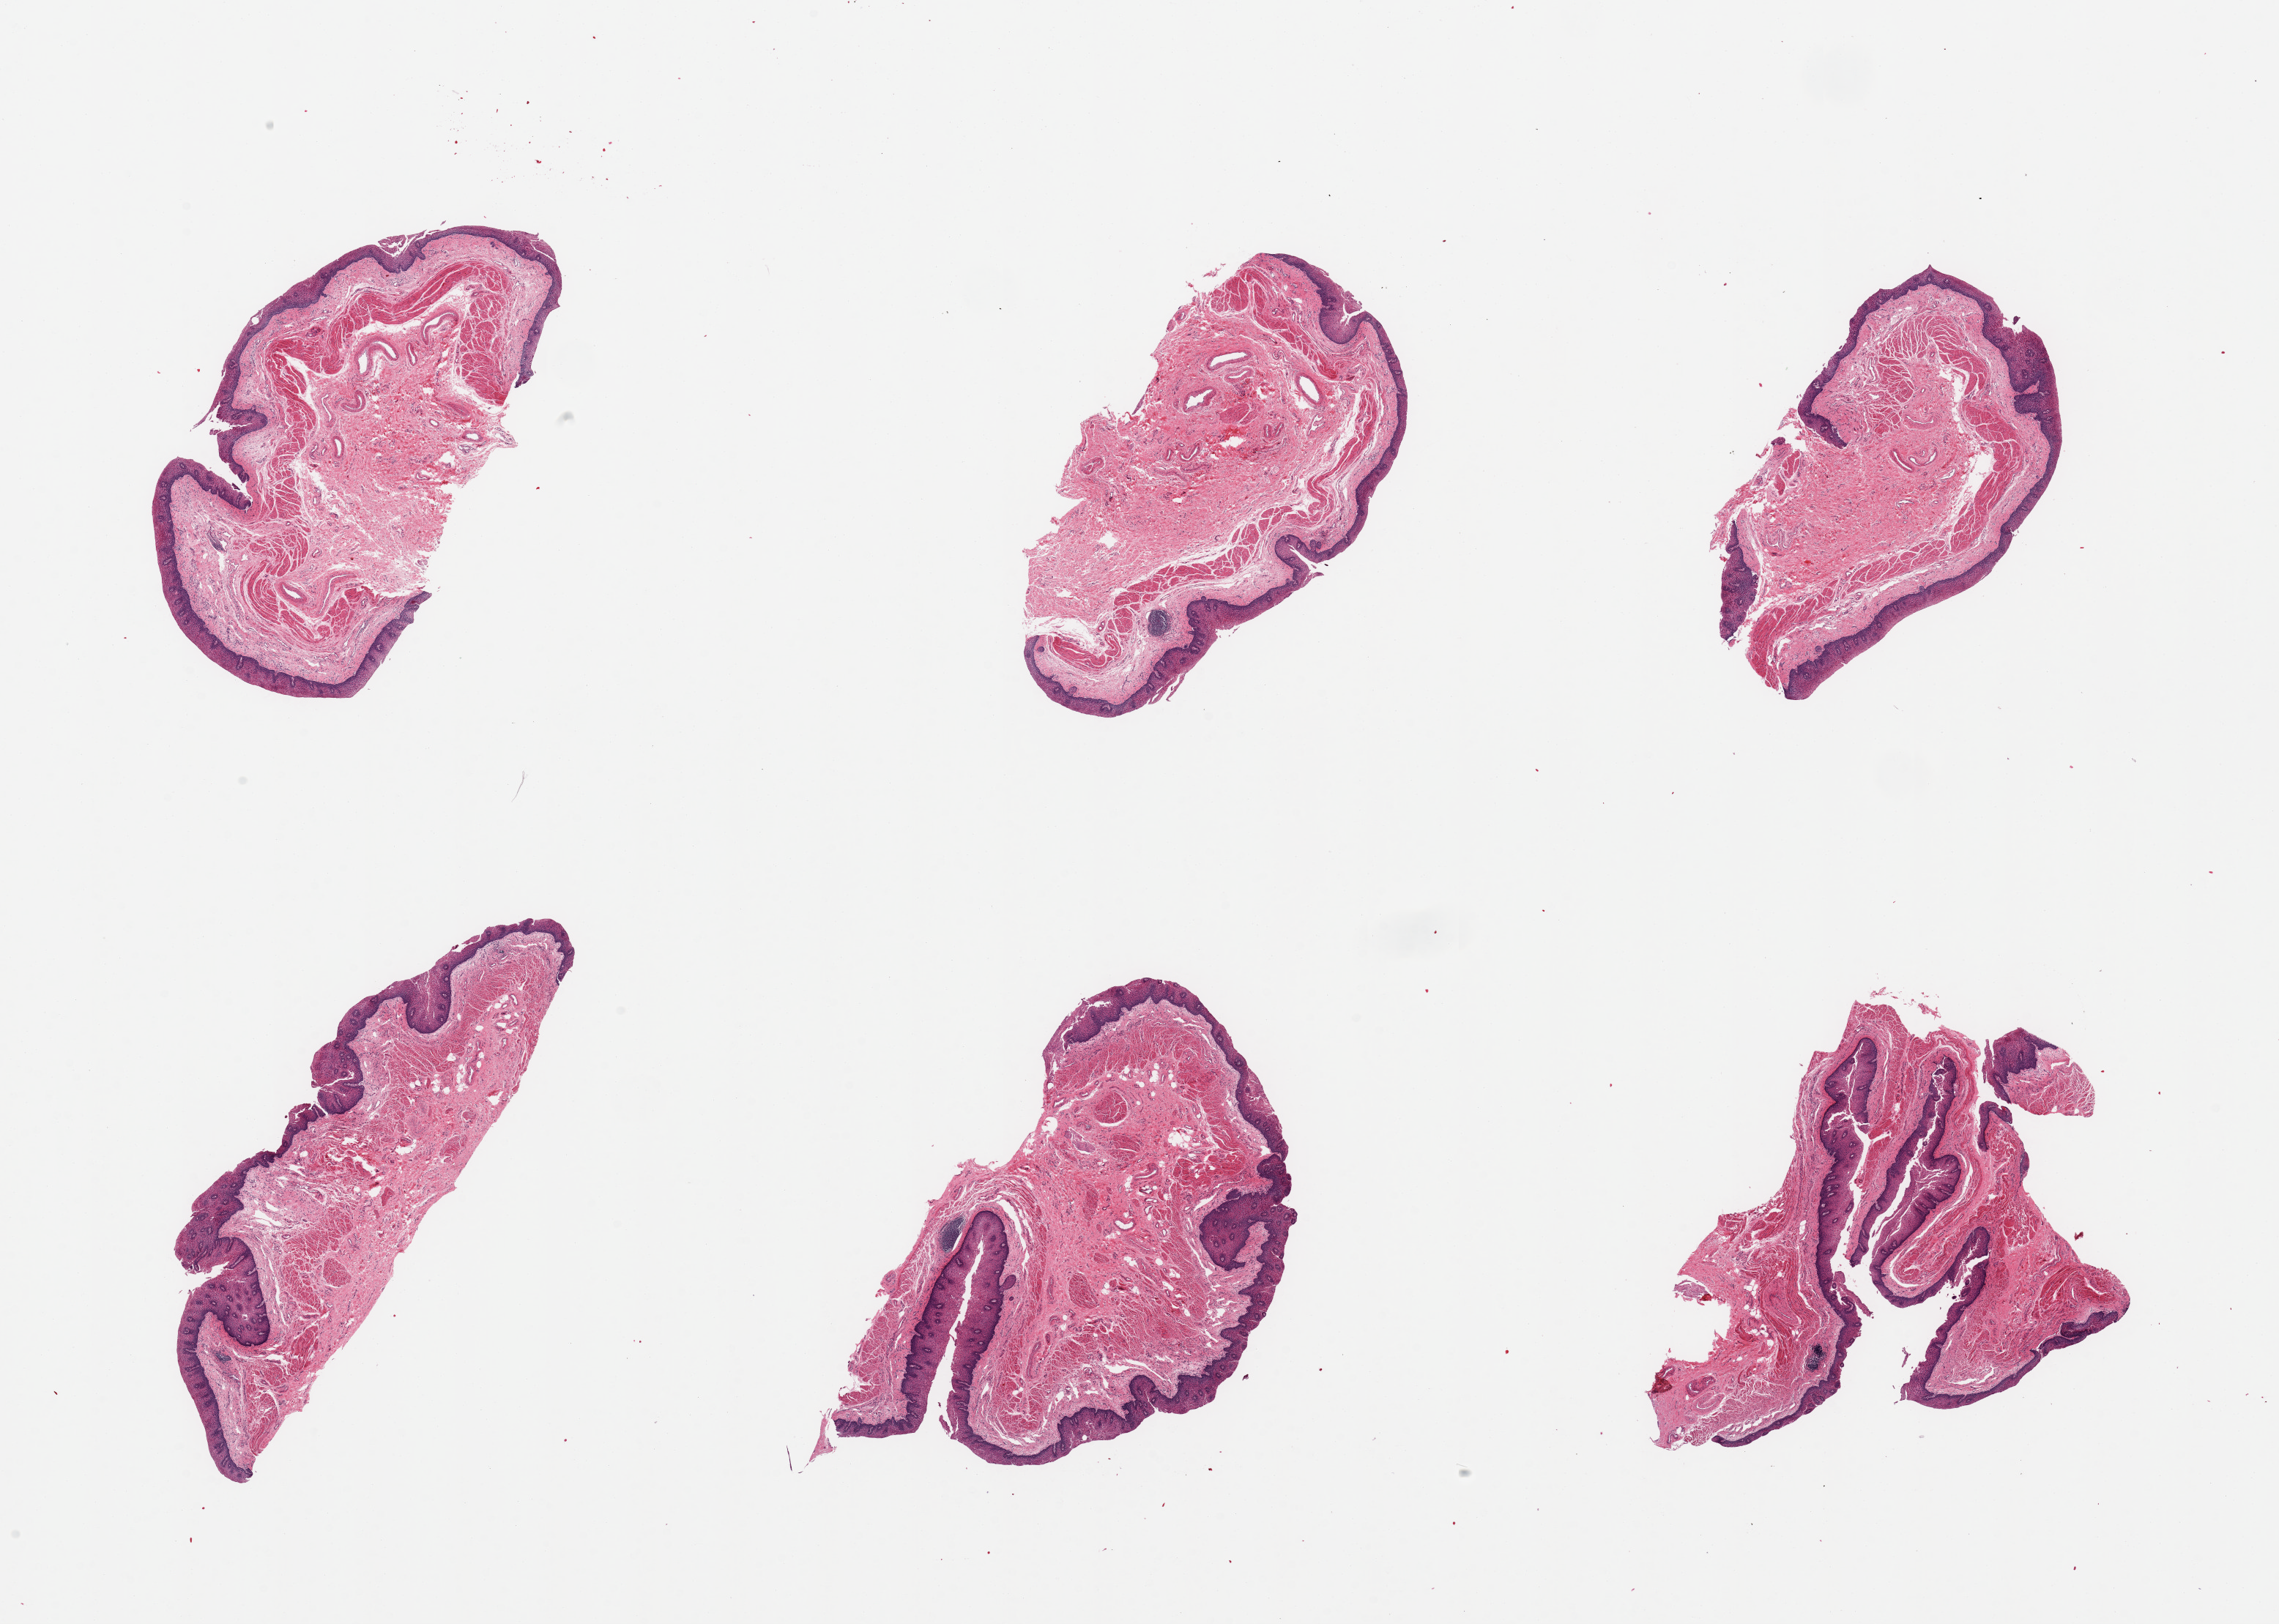
Haematoxylin and eosin whole-slide image — shown as a low-resolution overview of the whole scanned area (about 24.6 x 17.5 mm). PAXgene-fixed paraffin-embedded (PFPE) section. Section of esophageal mucous membrane (target tissue). Tissue donor sample.
- pathologist's review note for this sample: 6 pieces; well preserved mucosa and submucosa